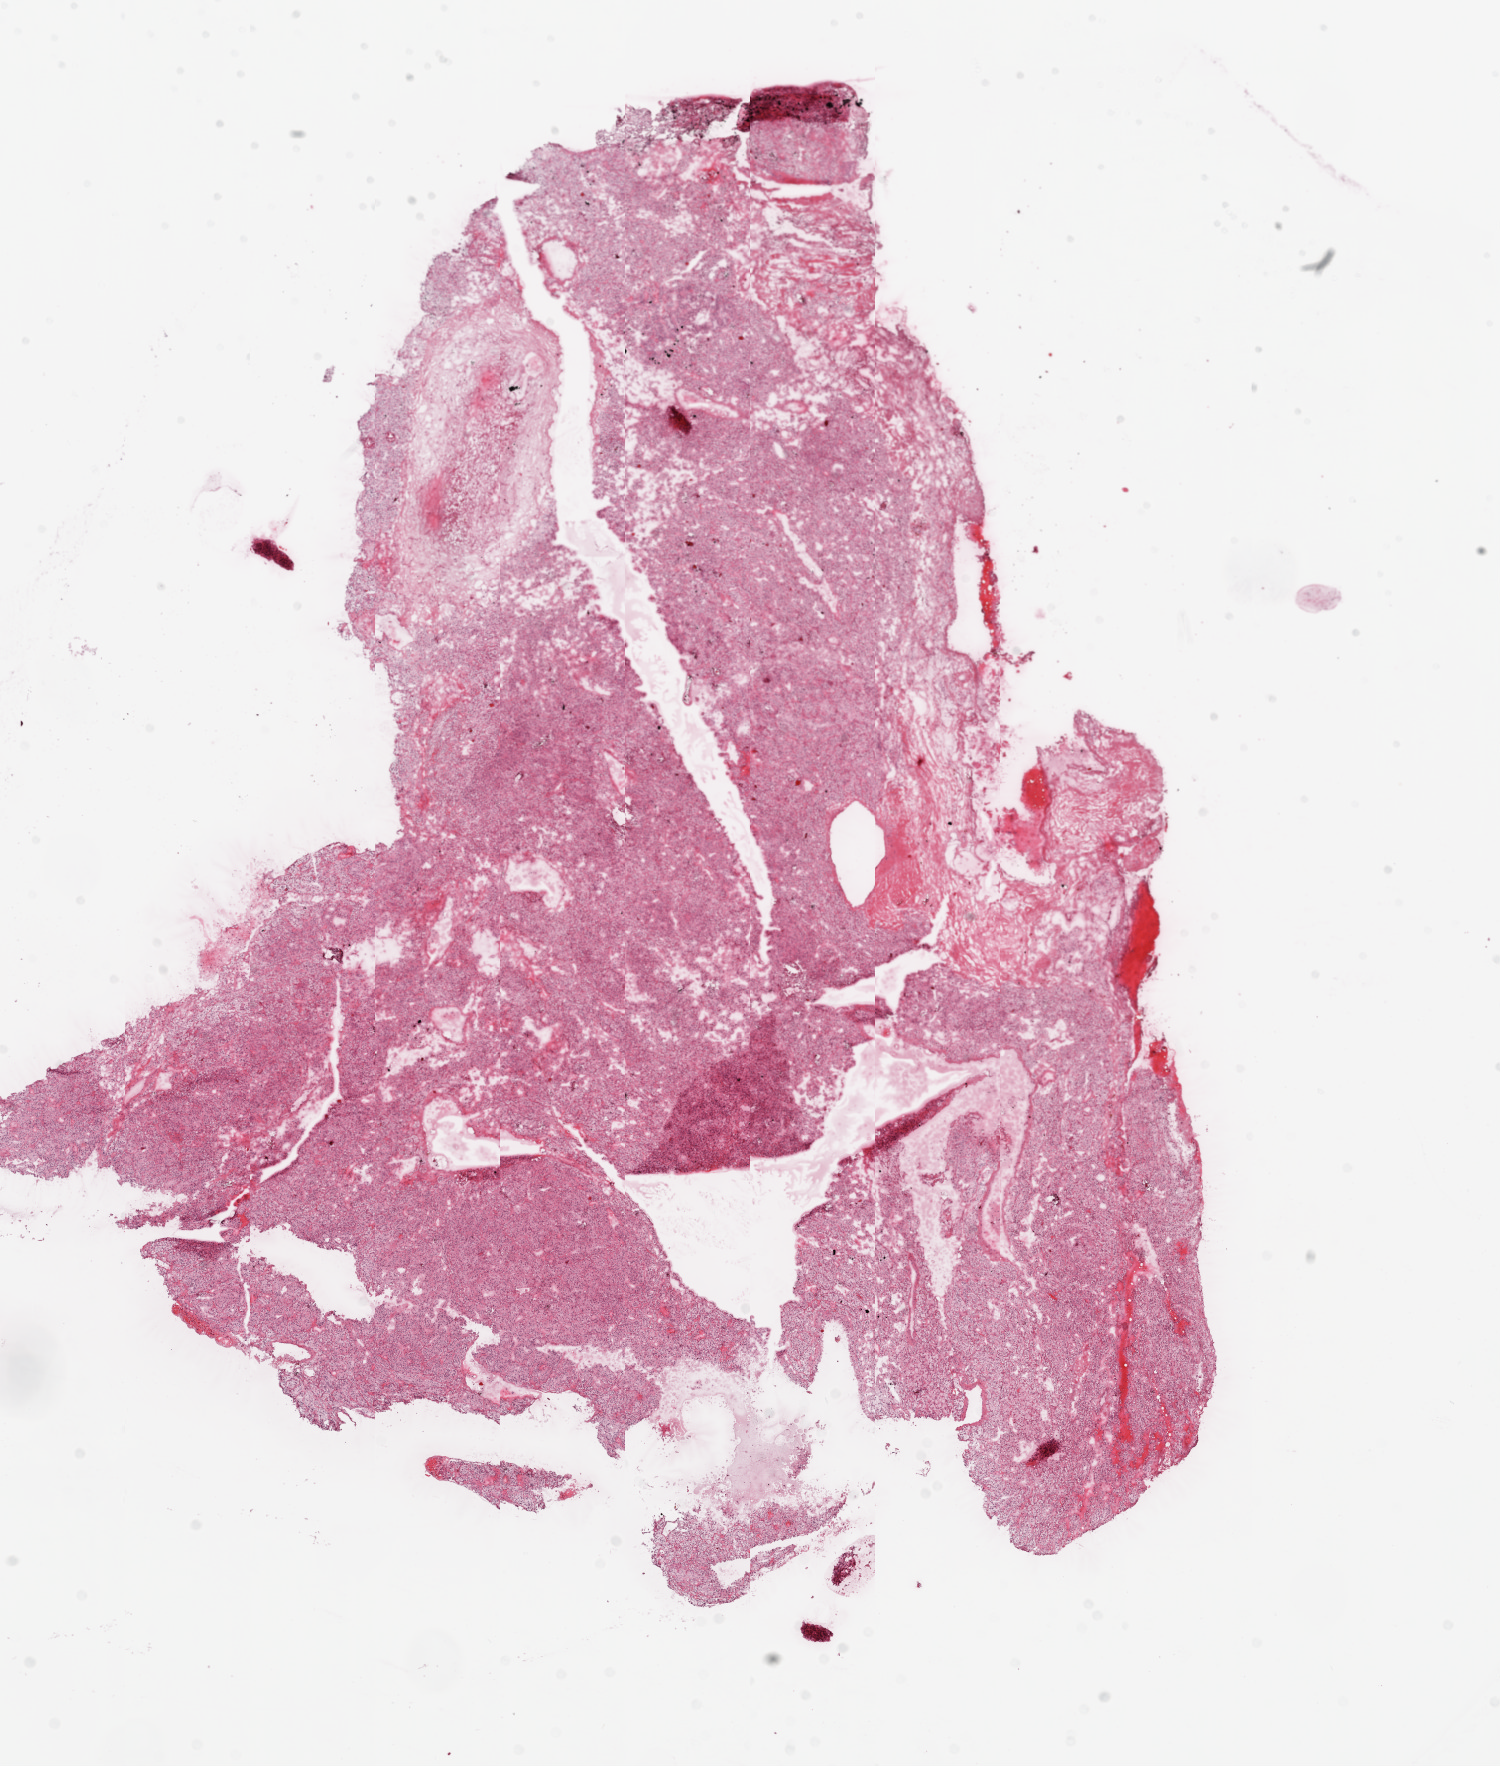
Whole-slide histology image, Hematoxylin and eosin (H&E) stained — low-resolution overview of the scanned area, about 12.0 x 14.2 mm. Frozen section. Kidney, primary tumour sample. Patient: male, age at initial diagnosis 68 years. Histologic grade: G3 (poorly differentiated). Pathologist review of this section (percent, as recorded): tumour cells 85%, tumour nuclei 85%, normal cells 0%, stromal cells 15%, necrosis 0%.
Laterality: right. Histologic diagnosis: Clear cell adenocarcinoma, NOS. AJCC pathologic stage: I. Lymph nodes positive (case pathology): 0 of 5 examined.